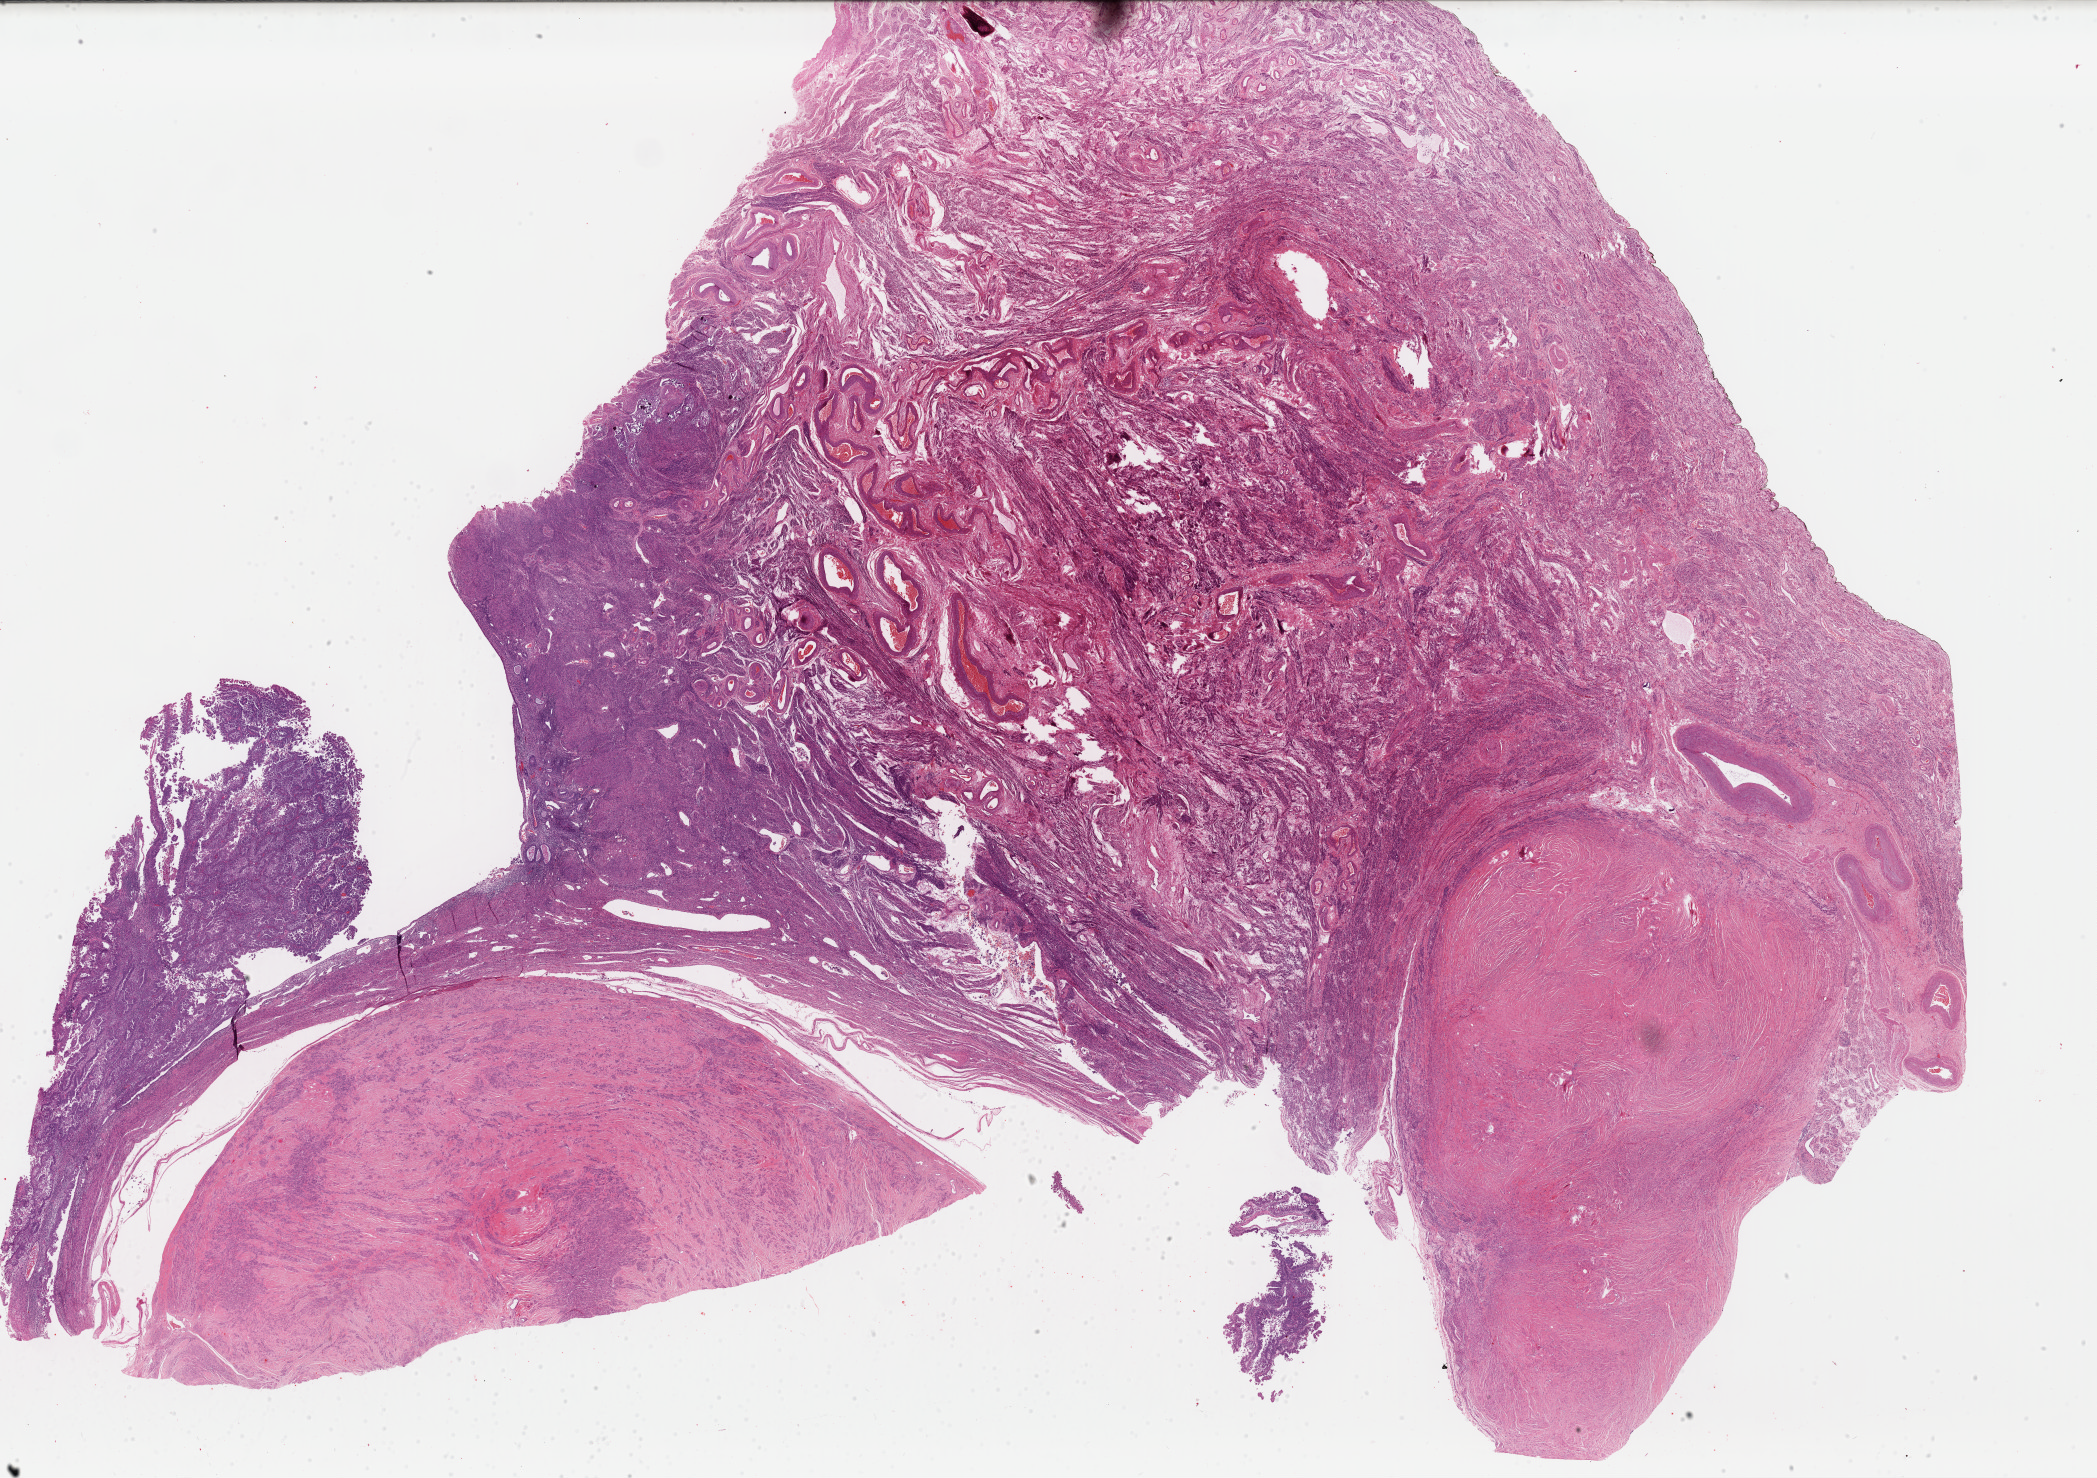
Whole-slide histology image, H&E-stained, a low-resolution overview of the entire scanned area, about 33.1 x 23.3 mm, formalin-fixed paraffin-embedded (FFPE) diagnostic section, primary tumour sample from the uterus. Female, age 65 years at initial diagnosis. Histologic grade: G3 (poorly differentiated).
- histologic diagnosis: Serous cystadenocarcinoma, NOS (endometrium)
- FIGO stage: IIIC2